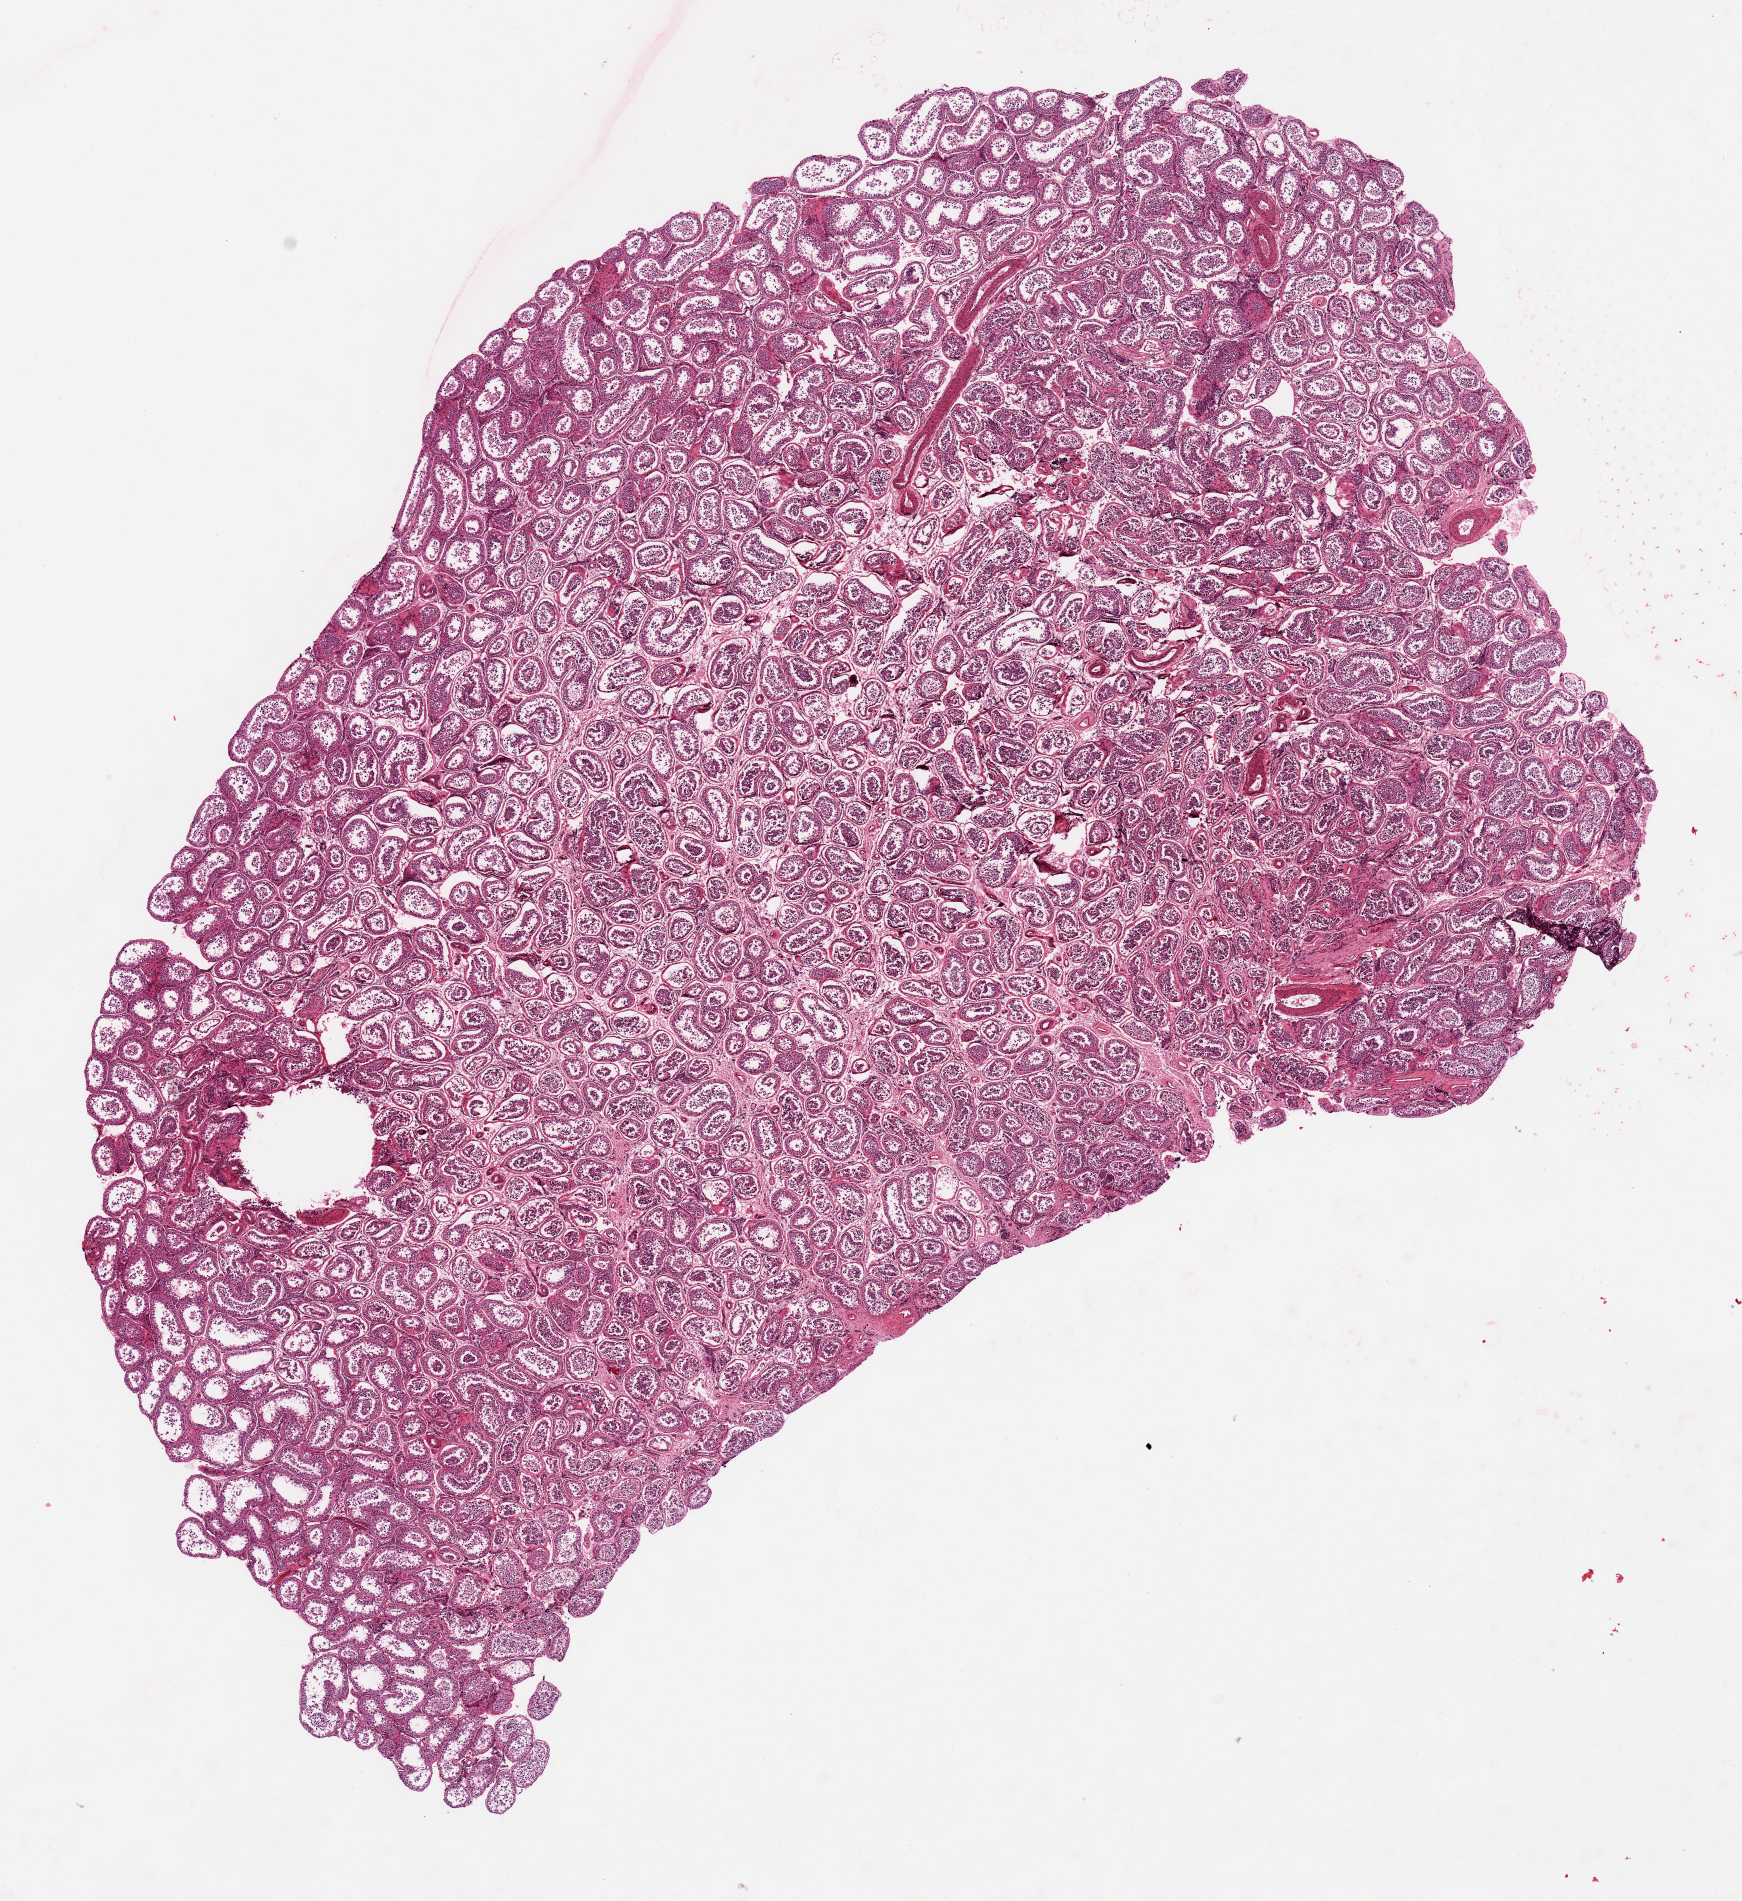
Whole-slide image, H&E stain, low-resolution overview of the scanned area, about 13.8 x 15.0 mm; PAXgene-fixed paraffin-embedded (PFPE) section; sampled site (target tissue): testis; tissue donor sample. Donor: male.
Pathologist's review note for this sample: Mild autolysis.